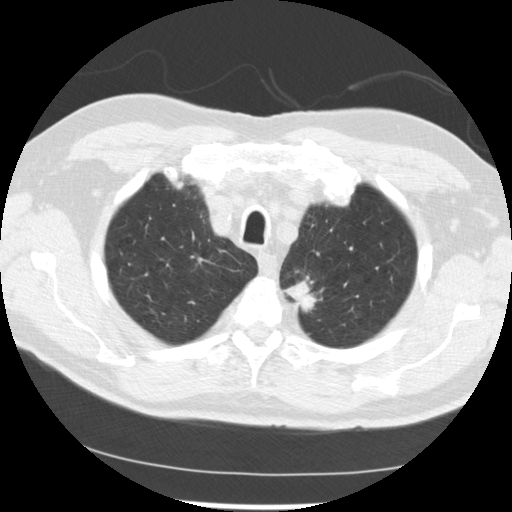
Axial slice from a low-dose chest CT screening exam. Baseline annual screen. Lung window (W 1500 / L -600 HU). 2.5 mm slice thickness. Standard (soft-tissue) reconstruction kernel (STANDARD). Slice 208 of 249 in the series. Male, age 71 years at enrolment. Current smoker at enrolment.
- Expert-annotated lung lesion, bounding box [x1, y1, x2, y2] px = [271, 269, 336, 319].
- The screening reader recorded 2 non-calcified nodules or masses ≥4 mm on this exam (left upper lobe, left upper lobe); which of them this box marks is not recorded.
- Official screen result: positive, change unspecified: nodule(s) >= 4 mm or enlarging nodule(s), mass(es), or other non-specific abnormalities suspicious for lung cancer.
- Lung cancer was diagnosed 37 days after this screen: adenocarcinoma, NOS, left upper lobe, poorly differentiated (G3), stage IIIB (AJCC 6th edition), 25 mm at pathology.